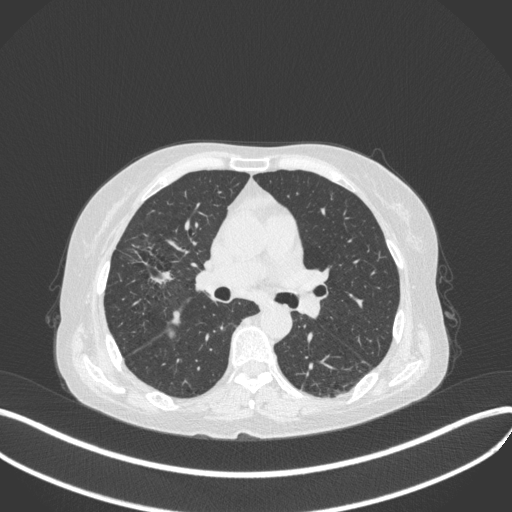
Chest CT, one axial slice. Position 231 of 429 along the scan axis. Reconstruction kernel B31f. Lung window (W 1500 / L -600 HU). 512 × 512 image matrix. Patient: female, 69 years. Case-level facts recorded for this patient, not image findings: clinical TNM (as recorded): T1b N3 M0.
Structures marked on this image (rectangle marked by the reading radiologist):
- lung tumour (recorded histology: small cell carcinoma): box from (x=126, y=238) to (x=178, y=289) px